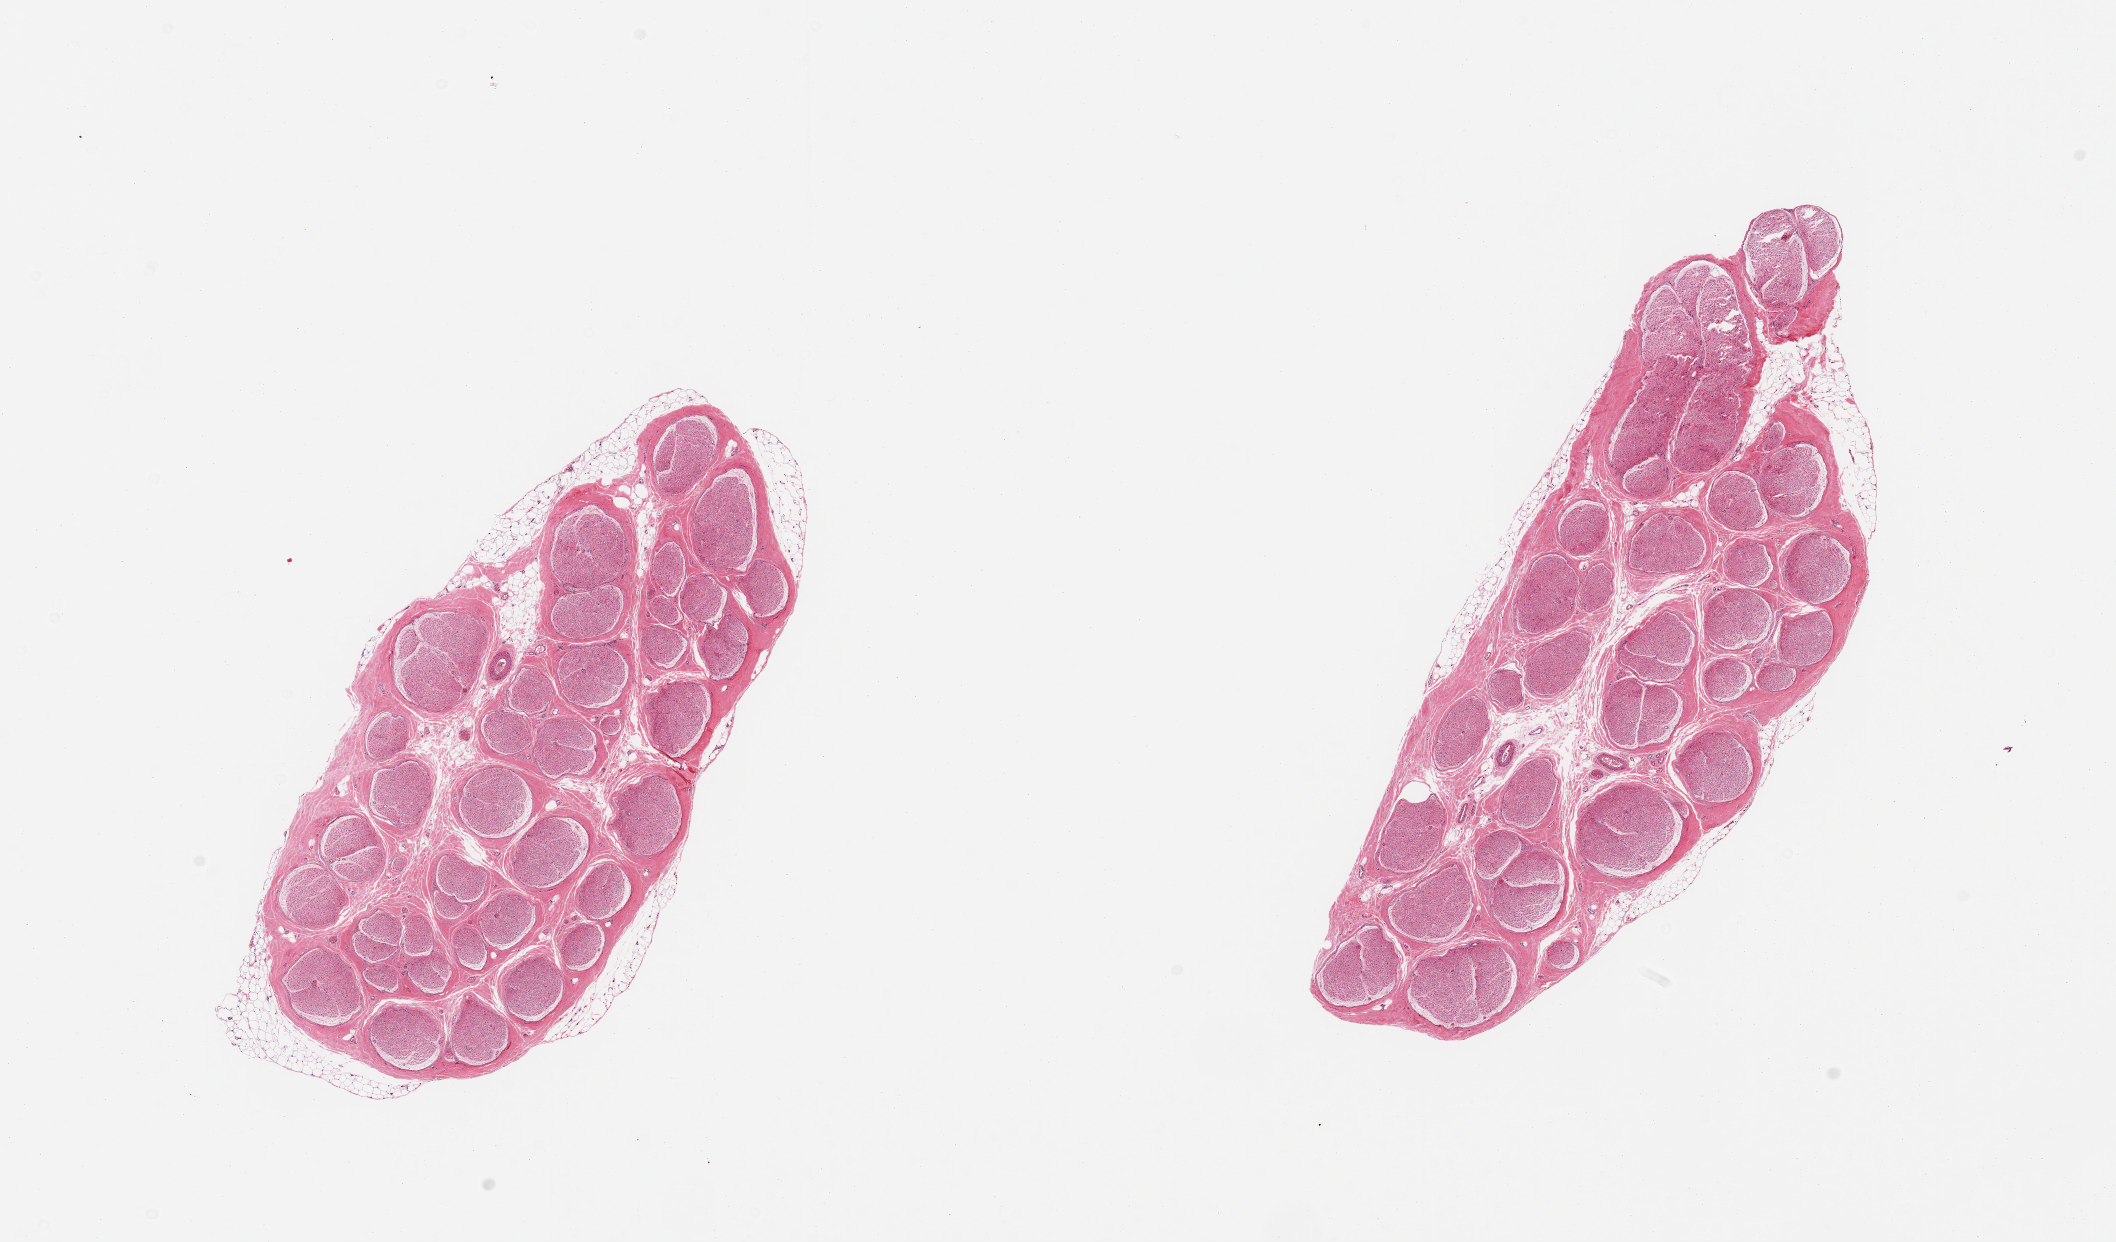
Whole-slide image, H&E stain, low-resolution overview of the scanned area, about 16.7 x 9.8 mm (slide scanned at 20x), PAXgene-fixed paraffin-embedded (PFPE) section, sampled site (target tissue): tibial nerve, donor tissue sample.
Reviewer comment on this tissue sample: 2 pieces, trace nubbin of adherent fat, ~0.2mm.